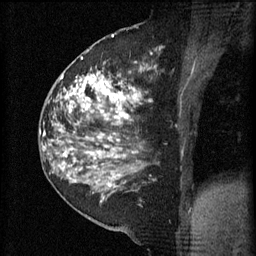
Breast MRI (dynamic contrast-enhanced), one sagittal slice. Slice 23 of 60 in the series (ordered by position). 3 images stored at this slice position (order not interpretable as contrast timing). 1.5 T. TE 4.2 ms, TR 11 ms. 256 × 256 image matrix, field of view 180 × 180 mm. Patient: female, 52 years.
Annotated regions visible in this slice (semi-automatically segmented with operator editing):
- analysis volume of interest (the breast-tissue region the enhancement analysis was run in; not a lesion): box from (x=81, y=52) to (x=154, y=157) px
- tumour enhancement mask (voxels above the 70 % enhancement threshold inside the analysis volume of interest): (x=81, y=58)–(x=140, y=157)